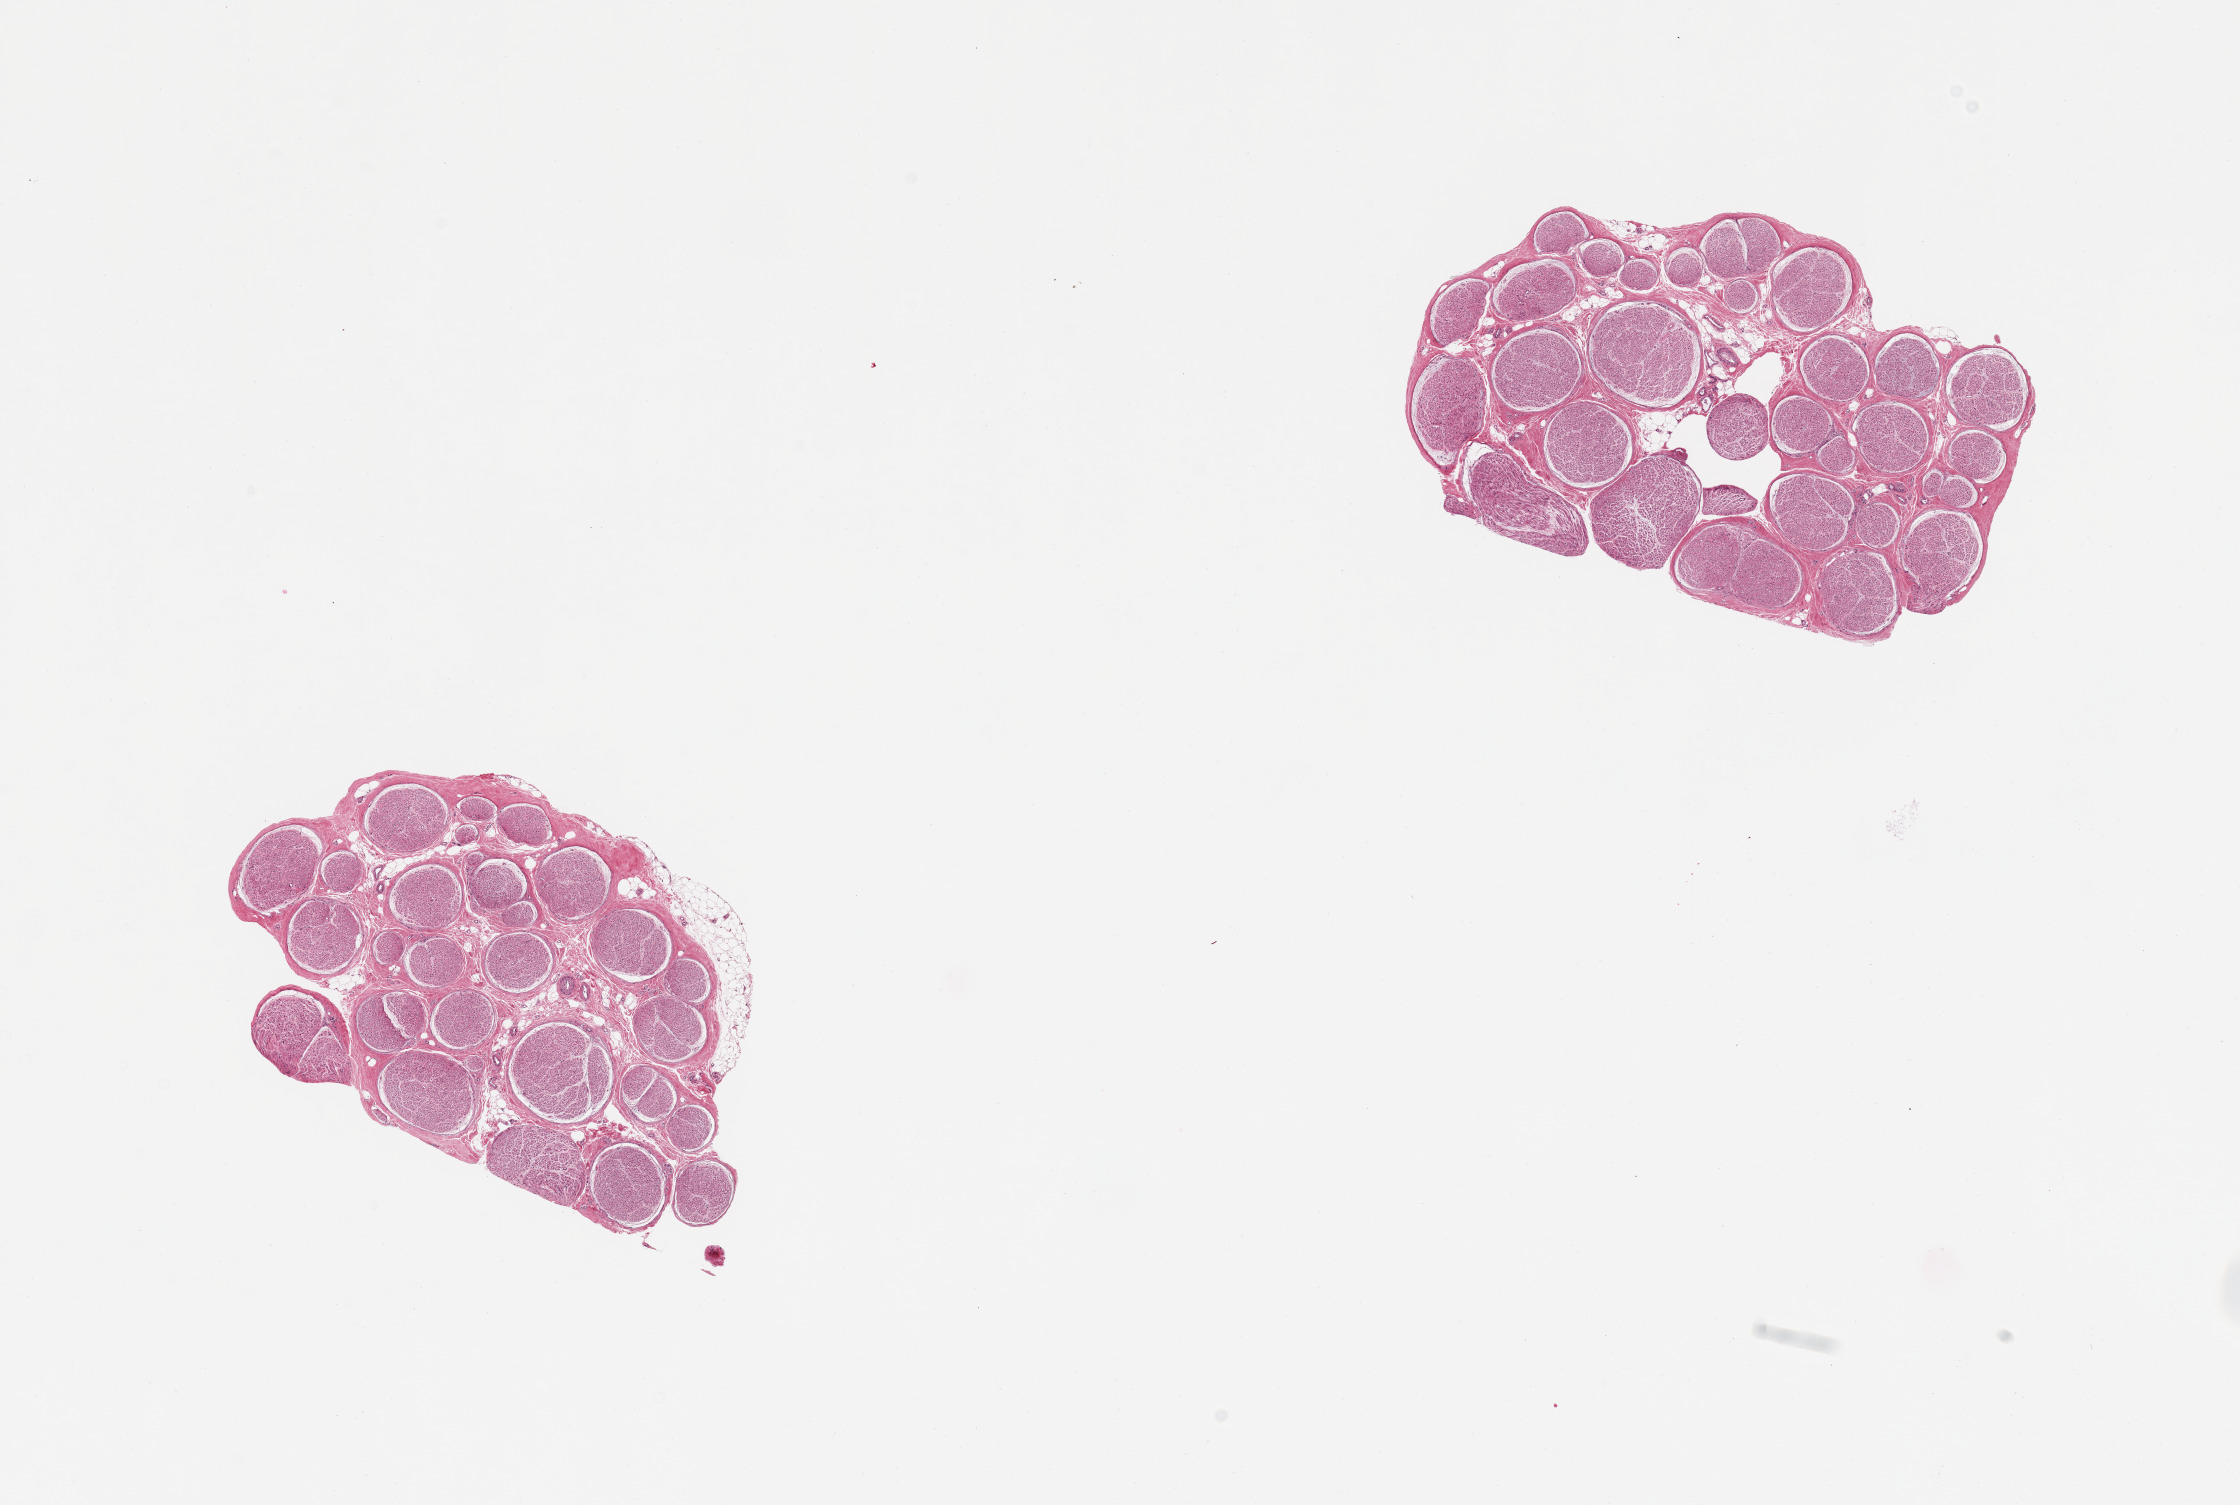
Haematoxylin and eosin whole-slide image, low-resolution overview of the scanned area, about 17.7 x 11.9 mm (slide scanned at 20x); PAXgene-fixed paraffin-embedded (PFPE) section; section of tibial nerve (target tissue); tissue donor sample. Donor: female.
Pathologist's review note for this sample: 2 pieces with minimal attached and internal fat.